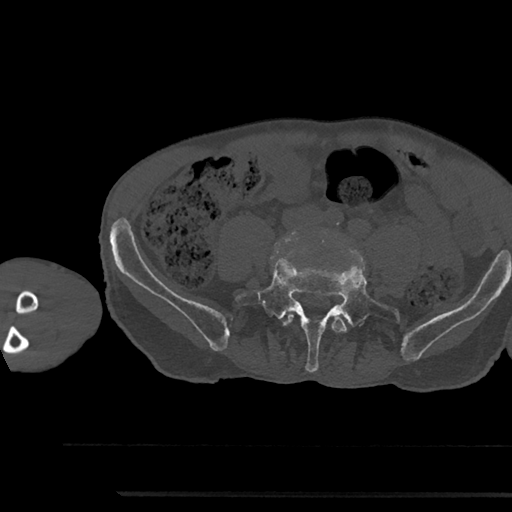
CT including the spine, one axial slice; slice 363 of 797 in the series (ordered by position); bone window (W 1800 / L 400 HU); 0.5 mm slice thickness; 512 × 512 image matrix. Male patient, age 79 years. Case-level facts recorded for this patient, not image findings: primary cancer: prostate.
Structures marked on this image (semi-automatically segmented with operator editing):
- L4 vertebra: box from (x=282, y=313) to (x=347, y=333) px
- L5 vertebra: (x=234, y=258)–(x=400, y=372)